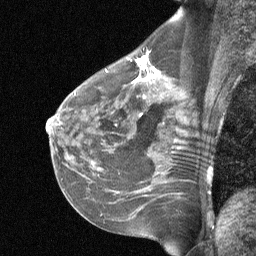
Breast MRI (dynamic contrast-enhanced), one sagittal slice. Position 38 of 64 along the scan axis. Dynamic contrast-enhanced study with each time point stored as its own series, time point 2 of 3 at this slice position (early post-contrast, ordered by acquisition time). 1.5 T. TE 4.8 ms, TR 27 ms. 2 mm slice thickness. 256 × 256 image matrix, field of view 200 × 200 mm. Female patient, age 51 years. Case-level facts recorded for this patient, not image findings: setting: breast cancer imaged before/during neoadjuvant chemotherapy; receptor status: HR-positive, HER2-negative.
Annotated regions visible in this slice (semi-automatically segmented with operator editing):
- analysis volume of interest (the breast-tissue region the enhancement analysis was run in; not a lesion): bounding box [x1, y1, x2, y2] px = [88, 42, 196, 119]
- tumour enhancement mask (voxels above the 90 % enhancement threshold inside the analysis volume of interest): [133, 56, 159, 82]